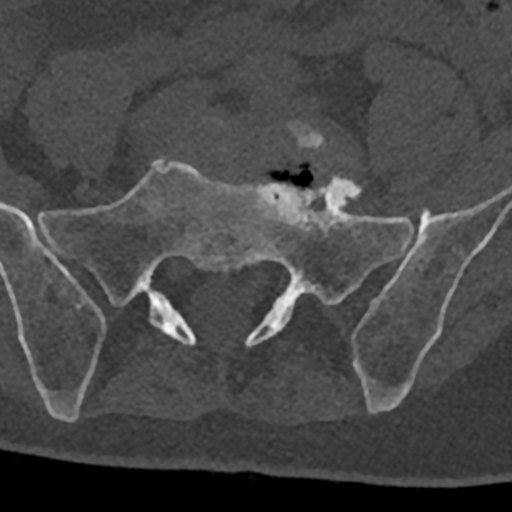
CT including the spine, one axial slice; slice 151 of 797 in the series (ordered by position); 120 kVp; bone window (W 1800 / L 400 HU); 0.5 mm slice thickness; 512 × 512 image matrix. Patient: male, 74 years. From the clinical record (not read from this slice): primary cancer: renal.
Outlined on this slice (semi-automatic segmentation, software-assisted and operator-edited):
- L5 vertebra: box from (x=220, y=121) to (x=325, y=150) px